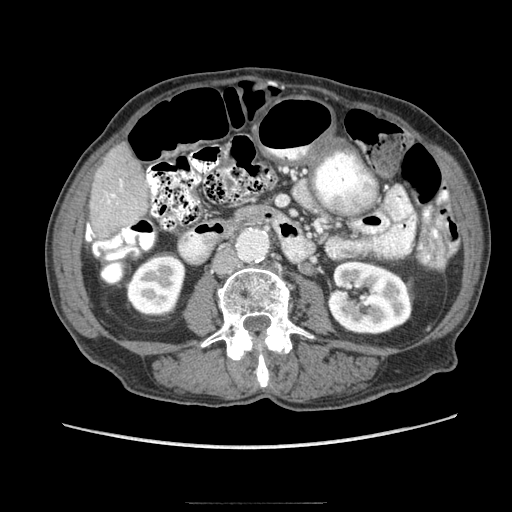
Contrast-enhanced abdominal CT (liver protocol), one axial slice. Position 18 of 83 along the scan axis. Reconstruction kernel STANDARD. Soft-tissue window (W 400 / L 40 HU). 2.5 mm slice thickness. 512 × 512 image matrix. Case-level facts recorded for this patient, not image findings: diagnosis: hepatocellular carcinoma (patient treated with transarterial chemoembolisation; whether this scan precedes or follows treatment is not stated here); TNM stage (as recorded): Stage-I; Child-Pugh class: A; tumour differentiation: moderately differentiated; tumour nodularity: uninodular.
Outlined on this slice (semi-automatically segmented with operator editing):
- liver parenchyma outside the tumour (the mass and vessels are separate outlines, so this box may not span the whole liver): bounding box [x1, y1, x2, y2] px = [90, 144, 148, 240]
- liver vessels: [93, 180, 123, 235]